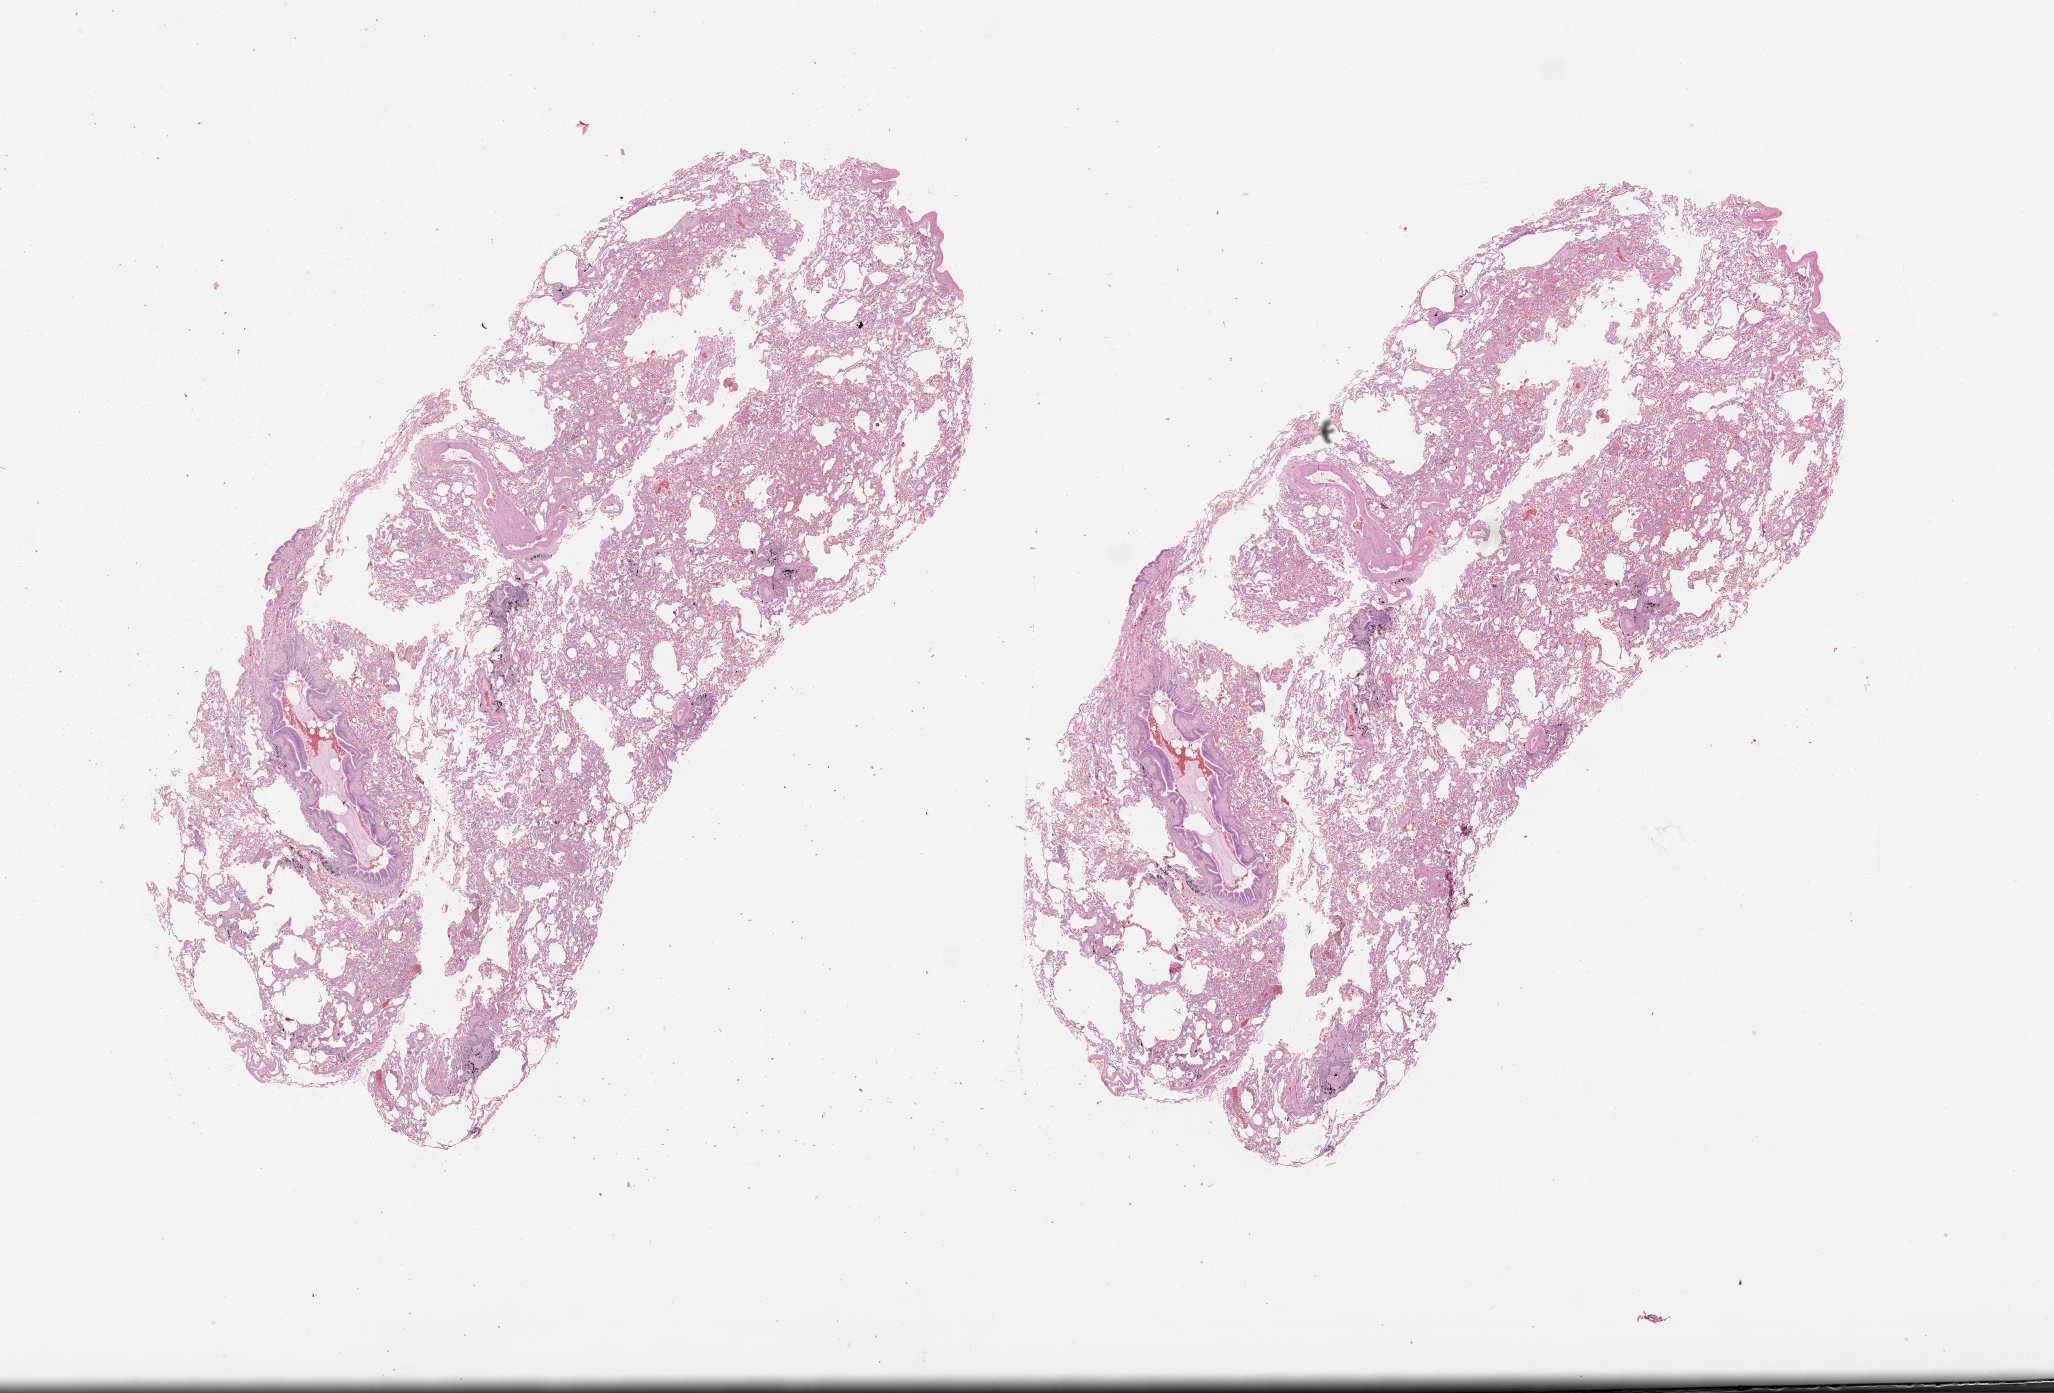
Digitized H&E tissue section (whole slide), shown as a low-resolution overview of the whole scanned area (about 33.1 x 22.4 mm), normal (non-tumour) tissue sample, lung. Male, 69 y/o.
- this section: normal (non-tumour) tissue from the same patient
- patient diagnosis (cohort enrolment): squamous cell carcinoma (lung)